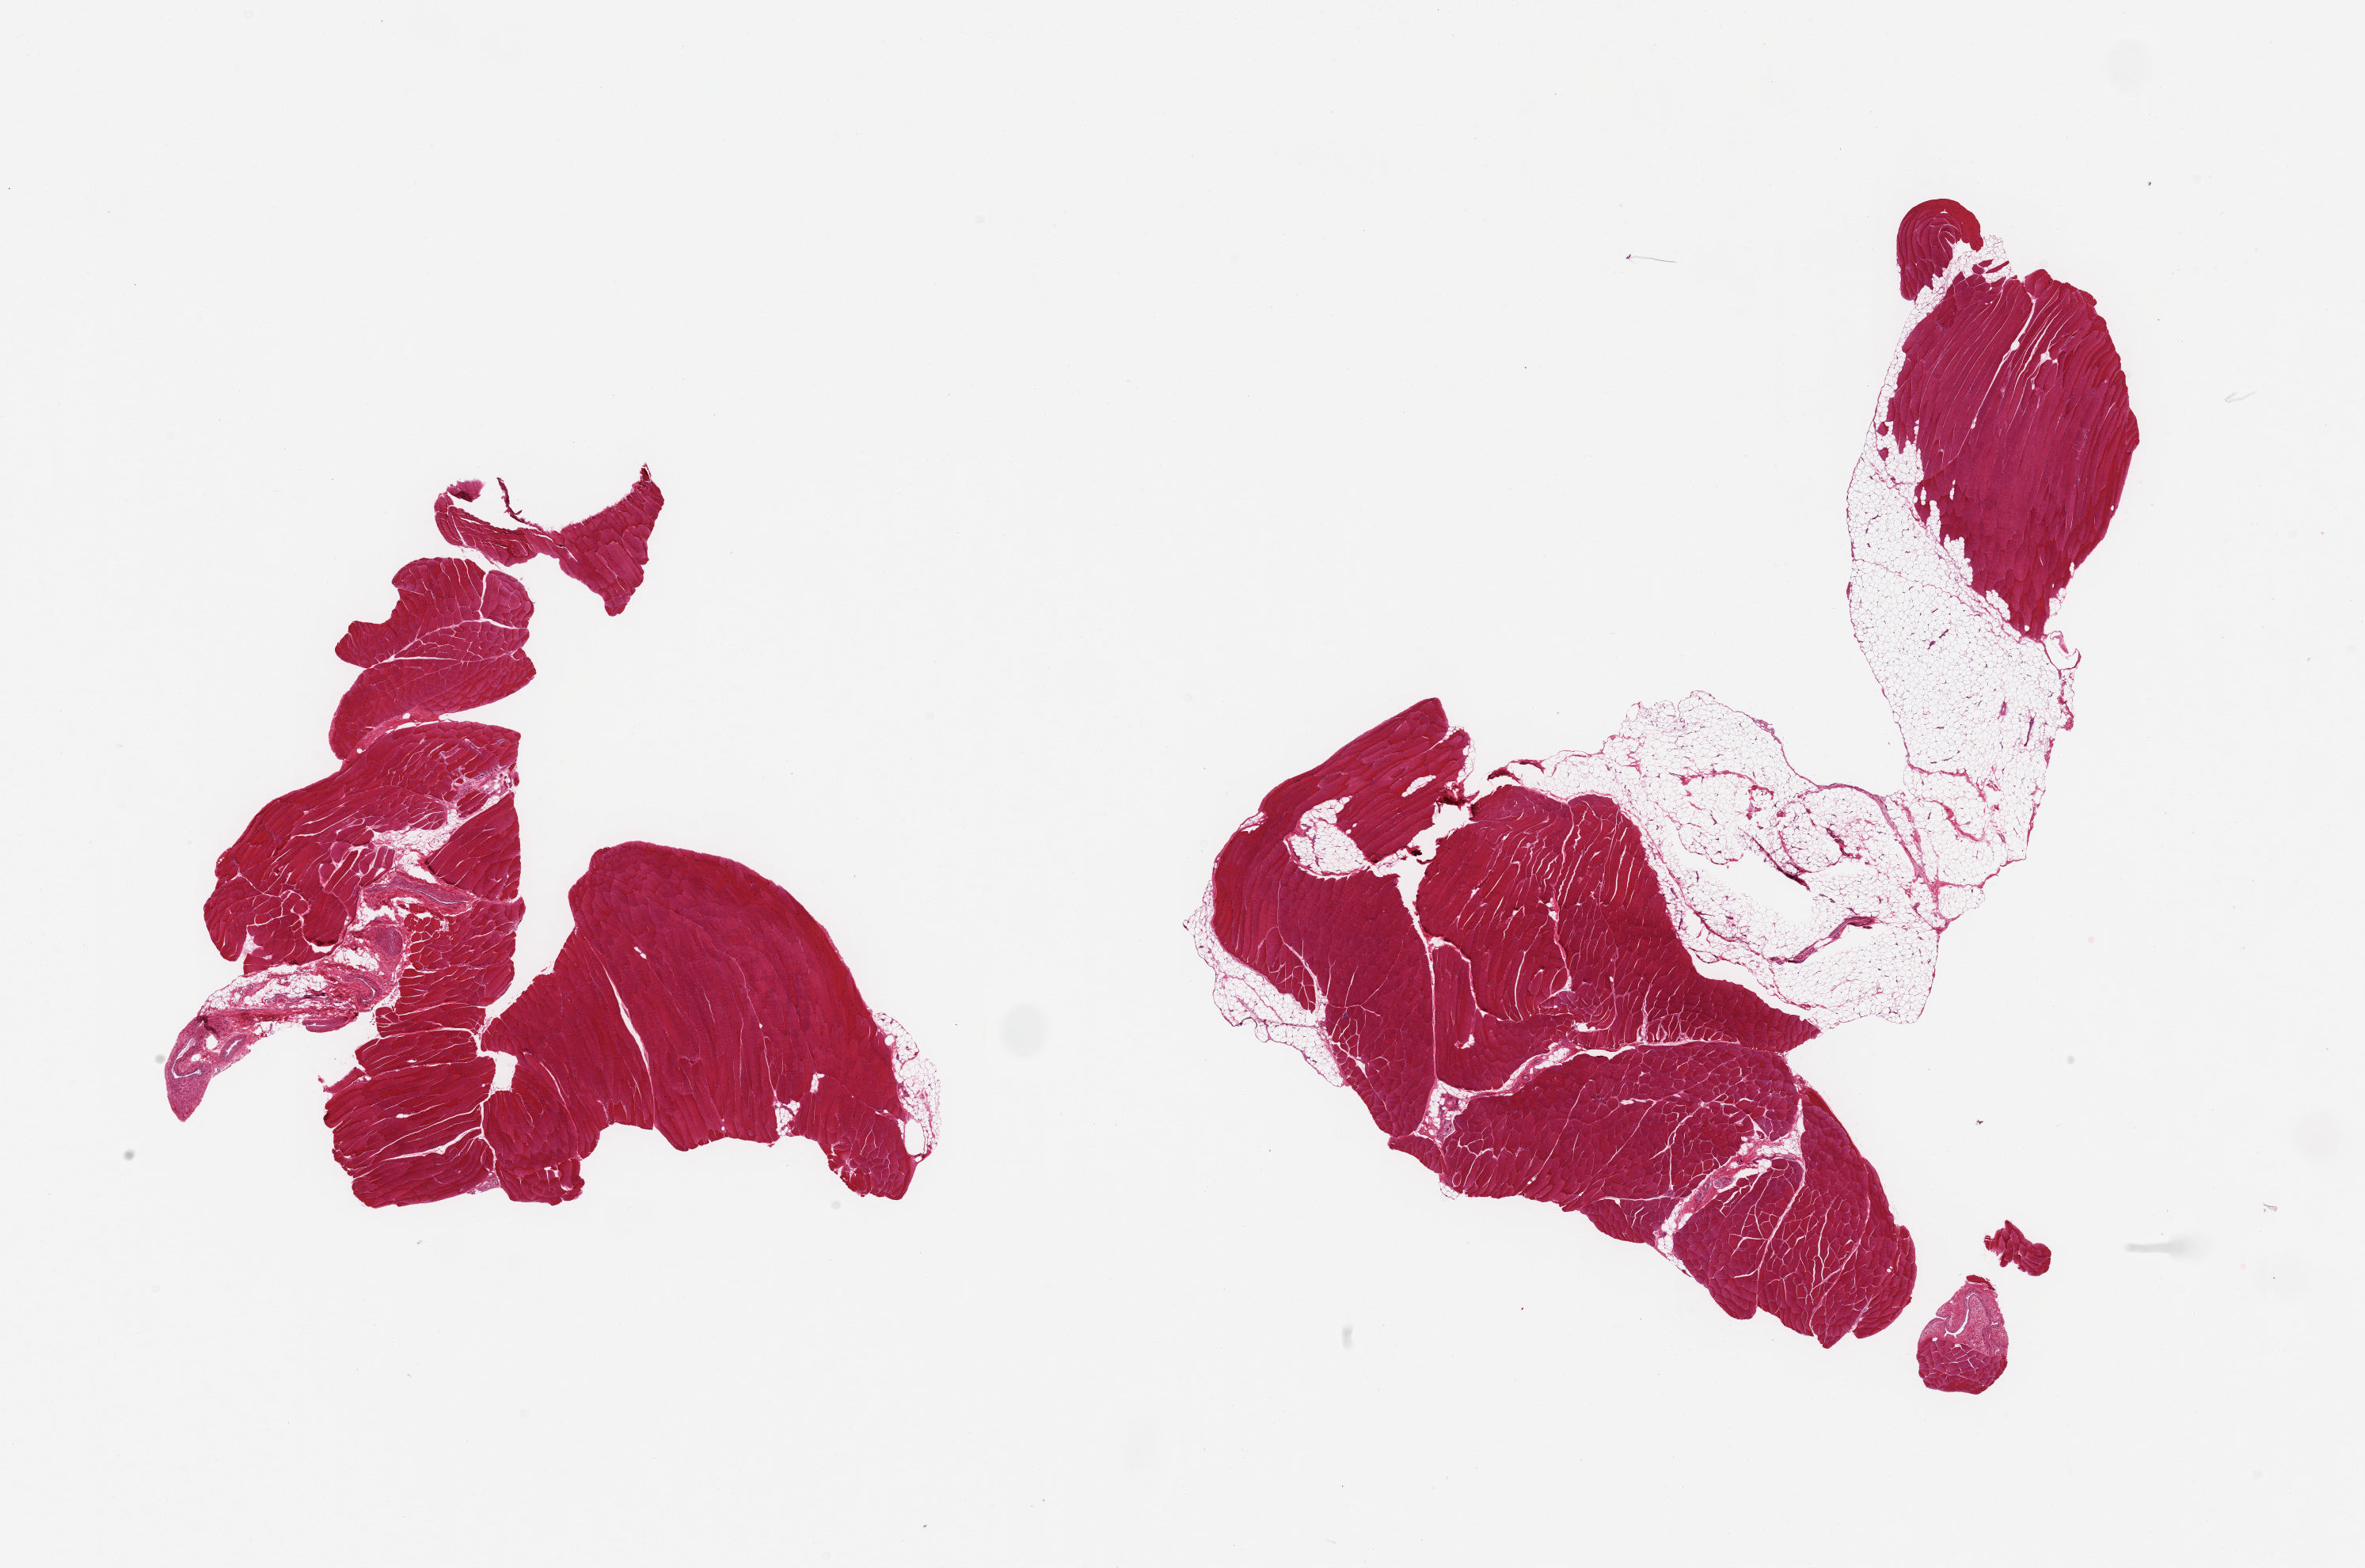
Hematoxylin and eosin (H&E) whole-slide image, whole scanned area (about 23.6 x 15.7 mm, acquisition: 20x scan) shown as a low-resolution overview, PAXgene-fixed paraffin-embedded (PFPE) section, section of skeletal muscle (target tissue), tissue donor sample. Female donor.
• reviewer comment on this tissue sample: 2 pieces; 1 piece has a large fatty band between 2 muscle bundles